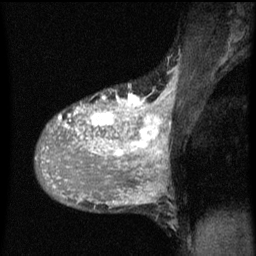
Breast MRI (dynamic contrast-enhanced), one sagittal slice; position 34 of 60 along the scan axis; dynamic contrast-enhanced series, image 2 of 3 at this slice position (ordered by acquisition); 1.5 T; TE 4.2 ms, TR 8 ms; 2 mm slice thickness; 256 × 256 image matrix. Female patient, age 36 years.
Structures marked on this image (semi-automatically segmented with operator editing):
- analysis volume of interest (the breast-tissue region the enhancement analysis was run in; not a lesion): bounding box [x1, y1, x2, y2] px = [38, 92, 167, 161]
- tumour enhancement mask (voxels above the 70 % enhancement threshold inside the analysis volume of interest): [42, 94, 167, 161]